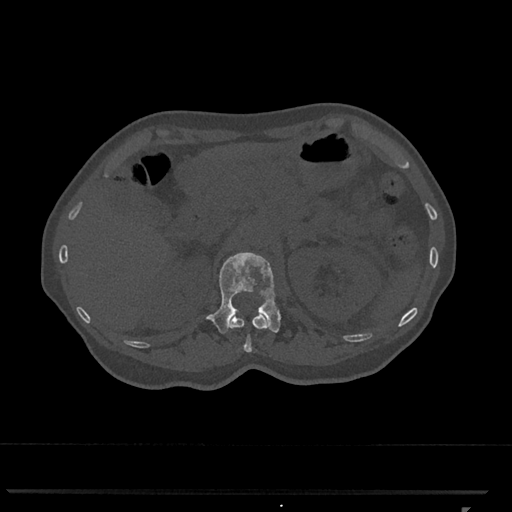
CT including the spine, one axial slice. Slice 422 of 793 in the series (ordered by position). Bone window (W 1800 / L 400 HU). 512 × 512 image matrix, field of view 380 × 380 mm. Female patient, age 62 years. From the clinical record (not read from this slice): primary cancer: renal.
Outlined on this slice (semi-automatic segmentation, software-assisted and operator-edited):
- L1 vertebra: bounding box [x1, y1, x2, y2] px = [206, 252, 281, 334]
- T12 vertebra: [230, 312, 267, 352]